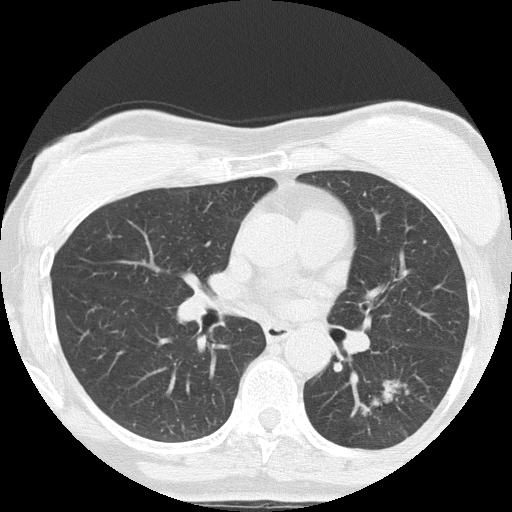
Chest CT (low-dose screening protocol), one axial image; third annual screen; lung window (W 1500 / L -600 HU); lung (sharp) reconstruction kernel (FC51); 120 kVp; slice 71 of 152 in the series. Female, age 64 years at enrolment. Former smoker at enrolment.
- Expert reader's lesion annotation, bounding box [x1, y1, x2, y2] px = [368, 363, 458, 440].
- The screening reader recorded 3 non-calcified nodules or masses ≥4 mm on this exam (right upper lobe, left lower lobe, right middle lobe); which of them this box marks is not recorded.
- Official screen result: positive, other.